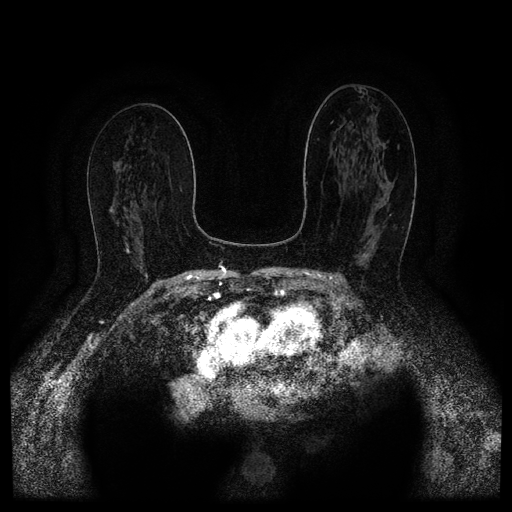
Breast MRI (dynamic contrast-enhanced, multi-phase), one axial slice; dynamic contrast-enhanced series, time point 2 of 5 at this slice position (early post-contrast); 1.5 T; TE 2.6 ms, TR 5.4 ms; 2 mm slice thickness; 512 × 512 image matrix. Patient: female, 67 years.
Outlined on this slice (semi-automatic segmentation, software-assisted and operator-edited):
- breast lesion (labelled 'tumour' in the annotation; benign lesions carry a separate 'benign' label): bounding box <362,251,370,261> (left, top, right, bottom; pixels)